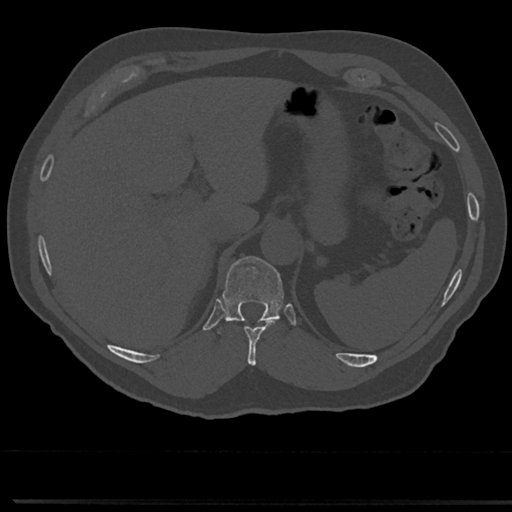
CT including the spine, one axial slice. Position 225 of 817 along the scan axis. Bone window (W 1800 / L 400 HU). 512 × 512 image matrix, field of view 355 × 355 mm. Patient: male, 61 years. Case-level facts recorded for this patient, not image findings: primary cancer: prostate.
Structures marked on this image (semi-automatic segmentation, software-assisted and operator-edited):
- T10 vertebra: bounding box <230,318,279,365> (left, top, right, bottom; pixels)
- T11 vertebra: <223,256,283,322>